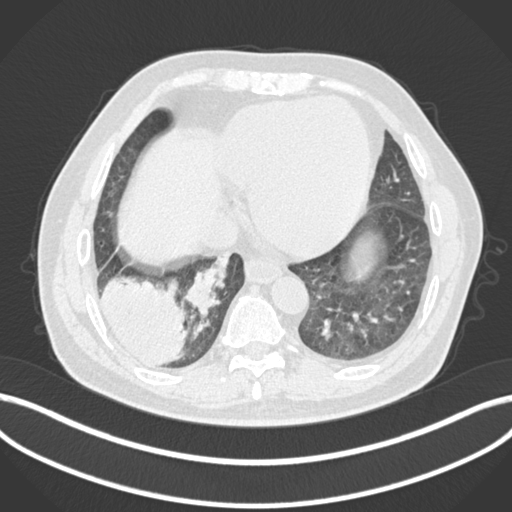
Chest CT, one axial slice. Slice 39 of 200 in the series (ordered by position). Reconstruction kernel B30f. Lung window (W 1500 / L -600 HU). 1 mm slice thickness. 512 × 512 image matrix, field of view 400 × 400 mm. Male patient, age 59 years.
Structures marked on this image (bounding box drawn by a radiologist):
- lung tumour (recorded histology: adenocarcinoma): bounding box <99,273,190,370> (left, top, right, bottom; pixels)